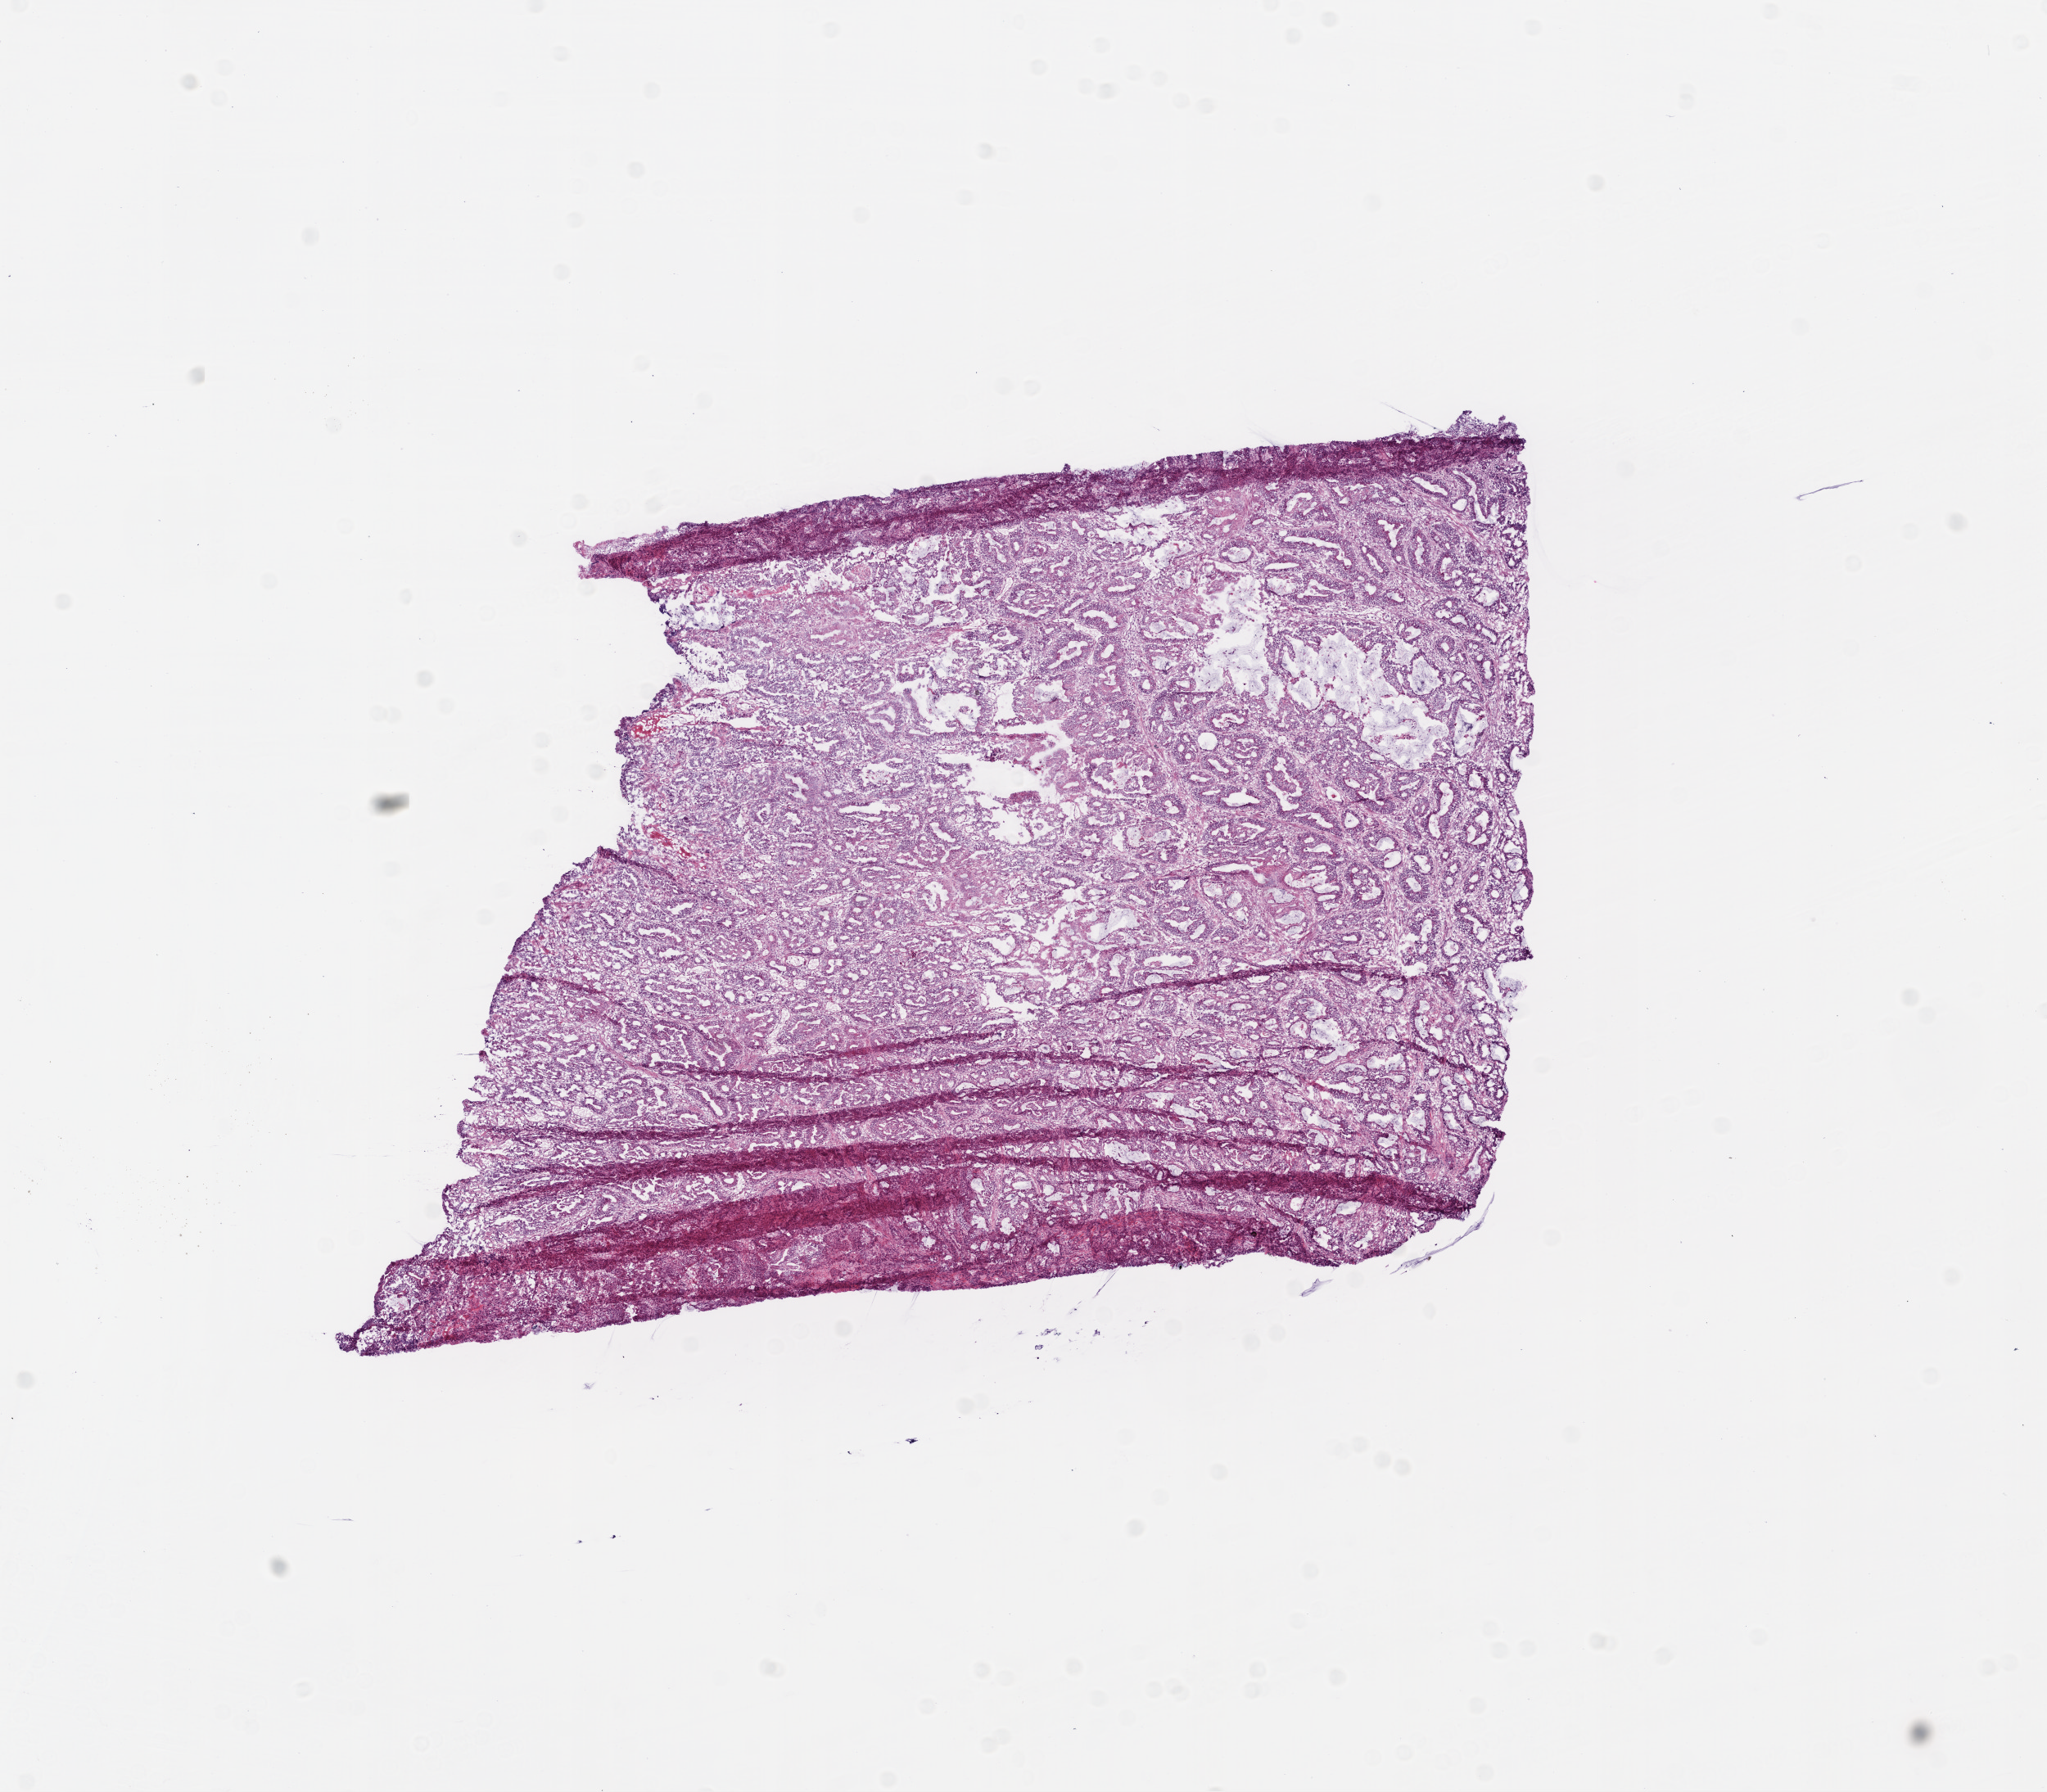
Whole-slide histology image, Hematoxylin and eosin (H&E) stained, low-resolution overview of the scanned area, about 10.0 x 8.8 mm (from a 20x scan), frozen section from the top of the tissue portion, sample: primary tumour, colon. Male, age 51 years at initial diagnosis. Slide review estimates, as recorded: tumour cells 87%, tumour nuclei 85%, normal cells 0%, stromal cells 10%, necrosis 3%.
AJCC pathologic stage: IIIA (6th edition). Histologic diagnosis: Adenocarcinoma, NOS. TNM: T2 N1 M0.